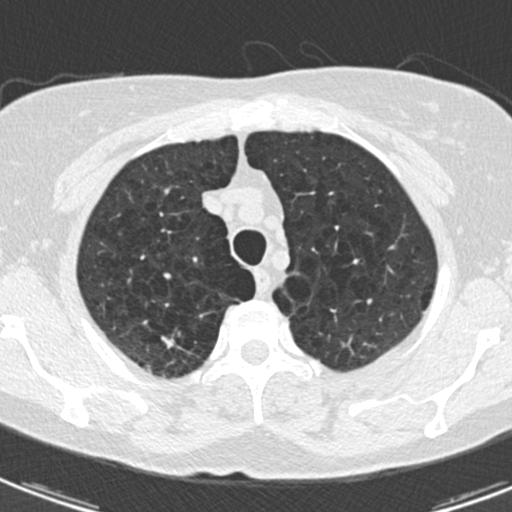
Low-dose screening chest CT, one axial slice; 120 kVp; lung window (W 1500 / L -600 HU); 2 mm slice thickness; 512 × 512 image matrix.
Structures marked on this image (manually delineated by an expert):
- lesion 1 (tumor, upper lobe of right lung): bounding box <160,336,175,348> (left, top, right, bottom; pixels)